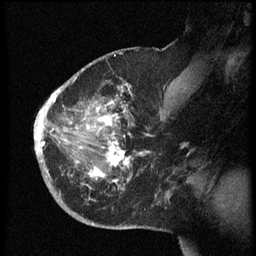
Breast MRI (dynamic contrast-enhanced), one sagittal slice. Position 39 of 60 along the scan axis. Dynamic contrast-enhanced series, image 2 of 3 at this slice position (ordered by acquisition). 1.5 T. TE 4.2 ms, TR 8.4 ms. 2.5 mm slice thickness. 256 × 256 image matrix, field of view 200 × 200 mm. Patient: female, 38 years. From the clinical record (not read from this slice): setting: breast cancer imaged before/during neoadjuvant chemotherapy; receptor status: HER2-positive.
Structures marked on this image (semi-automatic segmentation, software-assisted and operator-edited):
- analysis volume of interest (the breast-tissue region the enhancement analysis was run in; not a lesion): bounding box (x1, y1, x2, y2) in pixels: (35, 74, 173, 202)
- tumour enhancement mask (voxels above the 70 % enhancement threshold inside the analysis volume of interest): (35, 90, 132, 191)